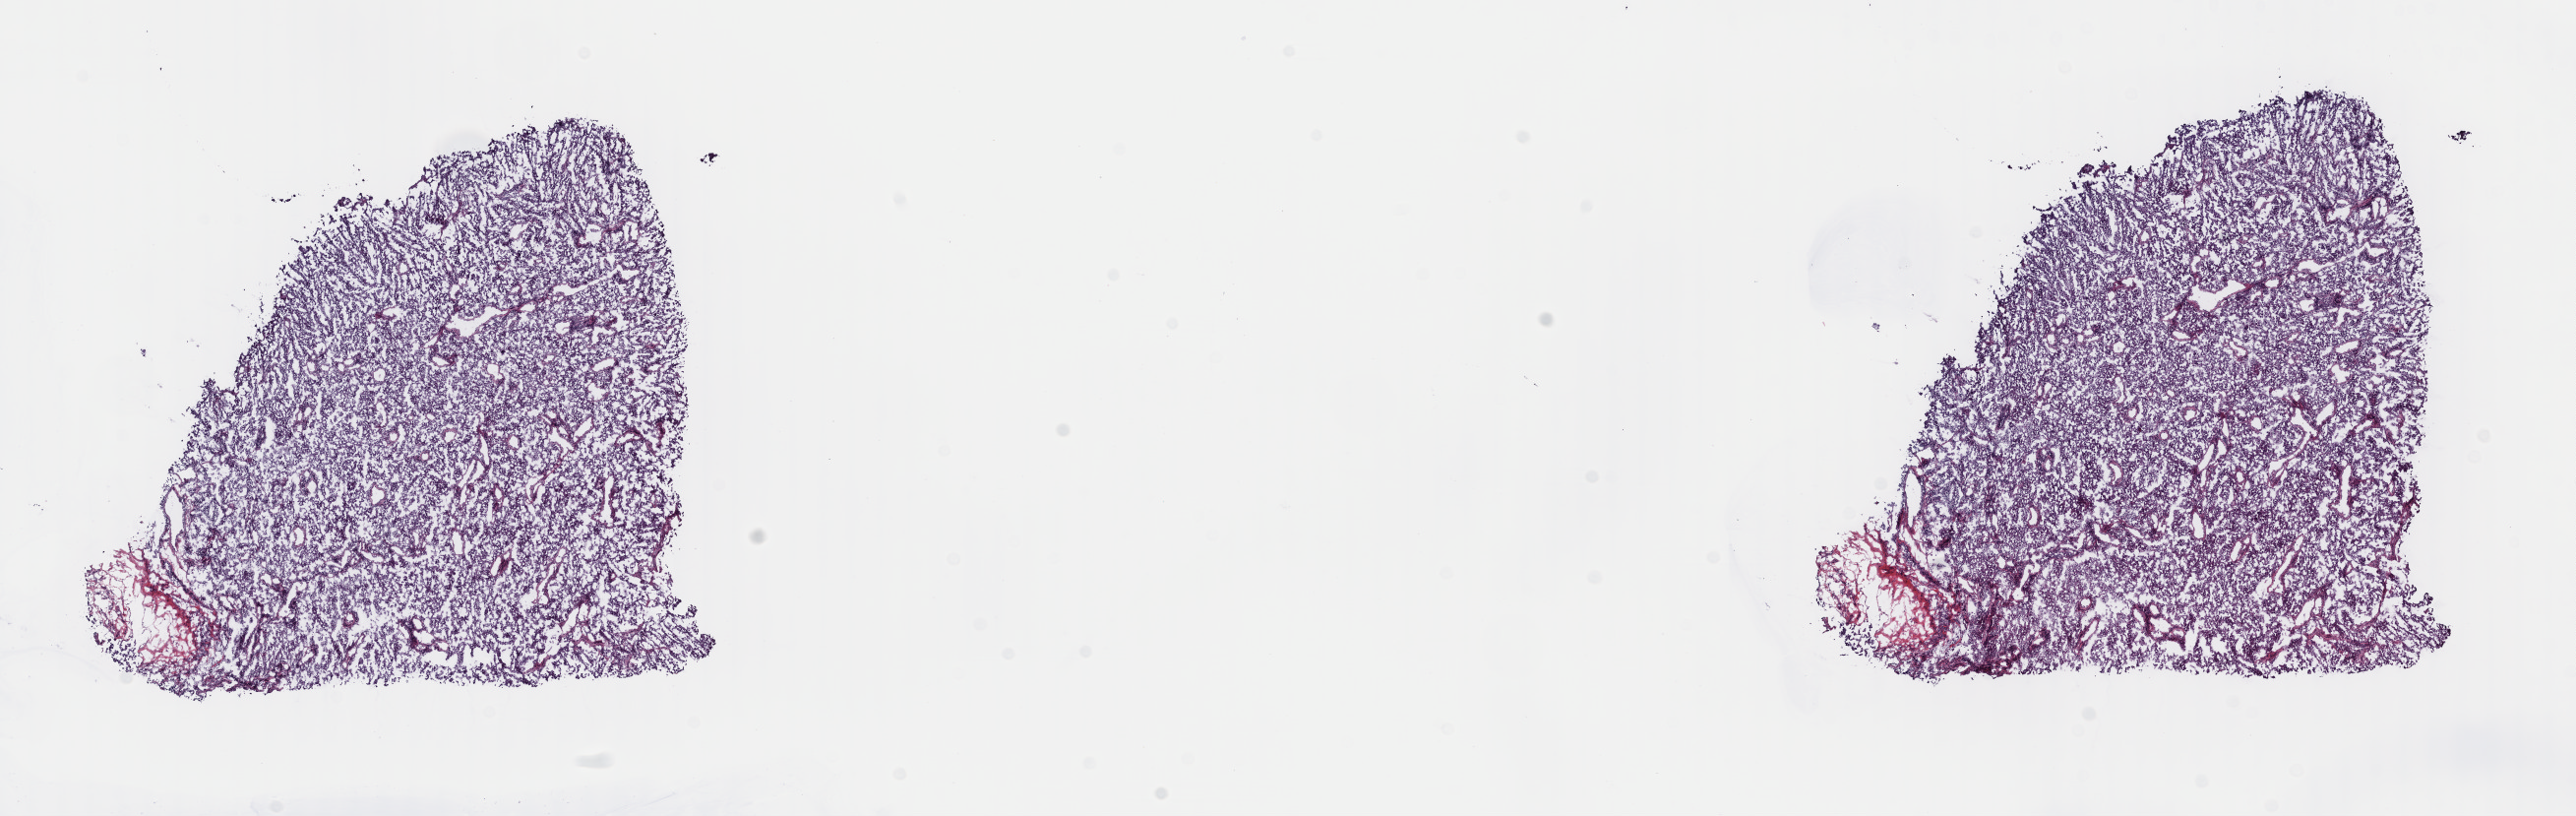
Digitized H&E tissue section (whole slide) — low-resolution overview of the scanned area, about 20.7 x 6.5 mm (acquisition: 40x scan). Frozen section from the top of the tissue portion. Sample: primary tumour, skin. Female patient; age at initial diagnosis 78 years. Slide review estimates, as recorded: tumour cells 100%, tumour nuclei 93%, normal cells 0%, stromal cells 0%, necrosis 0%. Infiltration values recorded for this section: lymphocyte infiltration 0%, monocyte infiltration 0%, neutrophil infiltration 0%.
- AJCC pathologic stage: IIIC (7th edition)
- histologic diagnosis: Amelanotic melanoma